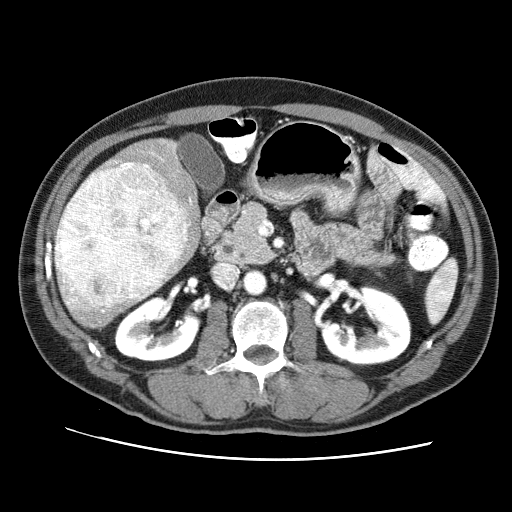
Contrast-enhanced abdominal CT (liver protocol), one axial slice. Slice 32 of 71 in the series (ordered by position). 120 kVp. Soft-tissue window (W 400 / L 40 HU). 512 × 512 image matrix, field of view 360 × 360 mm. Case-level facts recorded for this patient, not image findings: diagnosis: hepatocellular carcinoma (patient treated with transarterial chemoembolisation; whether this scan precedes or follows treatment is not stated here); TNM stage (as recorded): Stage-II; Child-Pugh class: A; tumour differentiation: well differentiated; tumour size: 4.6 cm.
Structures marked on this image (semi-automatic segmentation, software-assisted and operator-edited):
- liver parenchyma outside the tumour (the mass and vessels are separate outlines, so this box may not span the whole liver): box from (x=54, y=137) to (x=204, y=328) px
- mass: (x=55, y=162)–(x=191, y=324)
- liver vessels: (x=116, y=146)–(x=192, y=302)